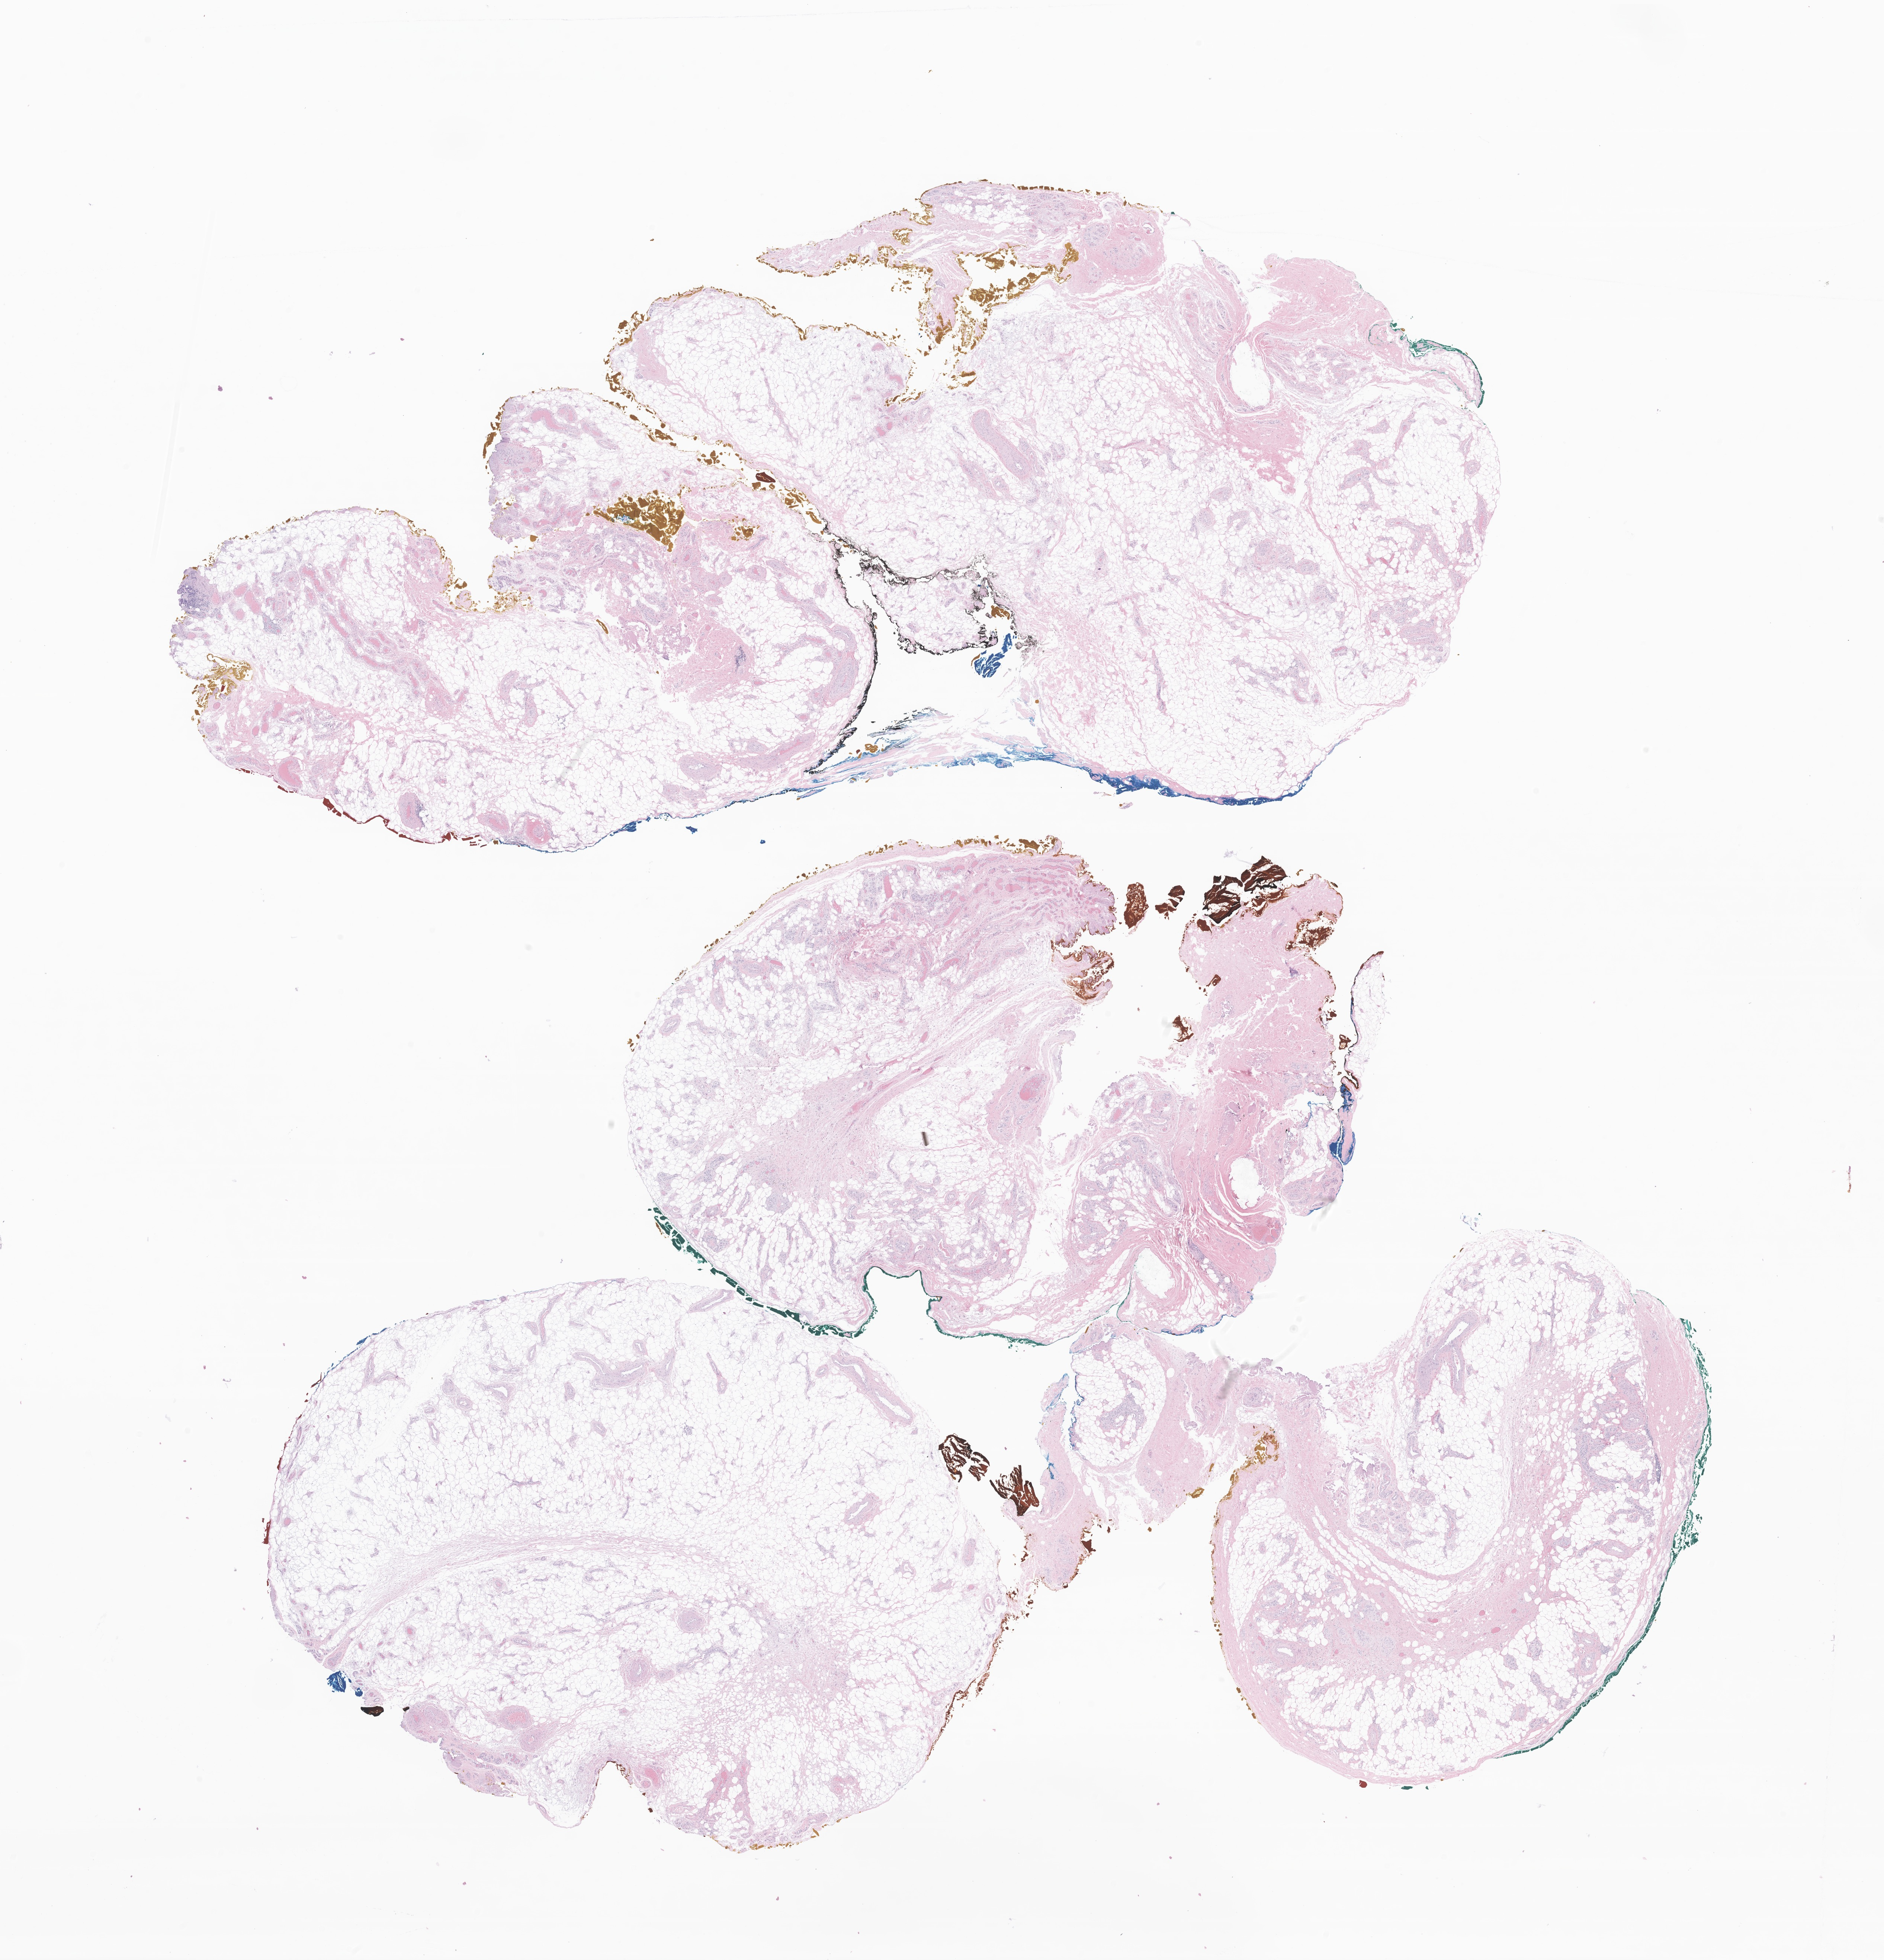
H&E whole-slide image of tumor tissue from the lower limb lymph node — low-resolution overview of the scanned area, about 21.4 x 22.2 mm, FFPE section. Male patient, age 190 months.
Recorded diagnosis: Malignant peripheral nerve sheath tumor, NOS.